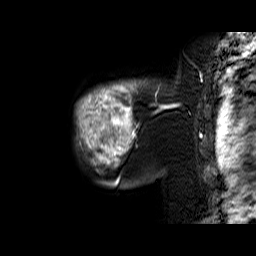
Breast MRI (dynamic contrast-enhanced), one sagittal slice; position 52 of 60 along the scan axis; dynamic contrast-enhanced series, time point 2 of 6 at this slice position (early post-contrast); 1.5 T; TE 6.4 ms, TR 32.9 ms; 4 mm slice thickness; 256 × 256 image matrix. Female patient. From the clinical record (not read from this slice): setting: breast cancer imaged before/during neoadjuvant chemotherapy; receptor status: triple-negative.
Outlined on this slice (semi-automatically segmented with operator editing):
- analysis volume of interest (the breast-tissue region the enhancement analysis was run in; not a lesion): bounding box <77,80,159,174> (left, top, right, bottom; pixels)
- tumour enhancement mask (voxels above the 100 % enhancement threshold inside the analysis volume of interest): <77,80,159,168>